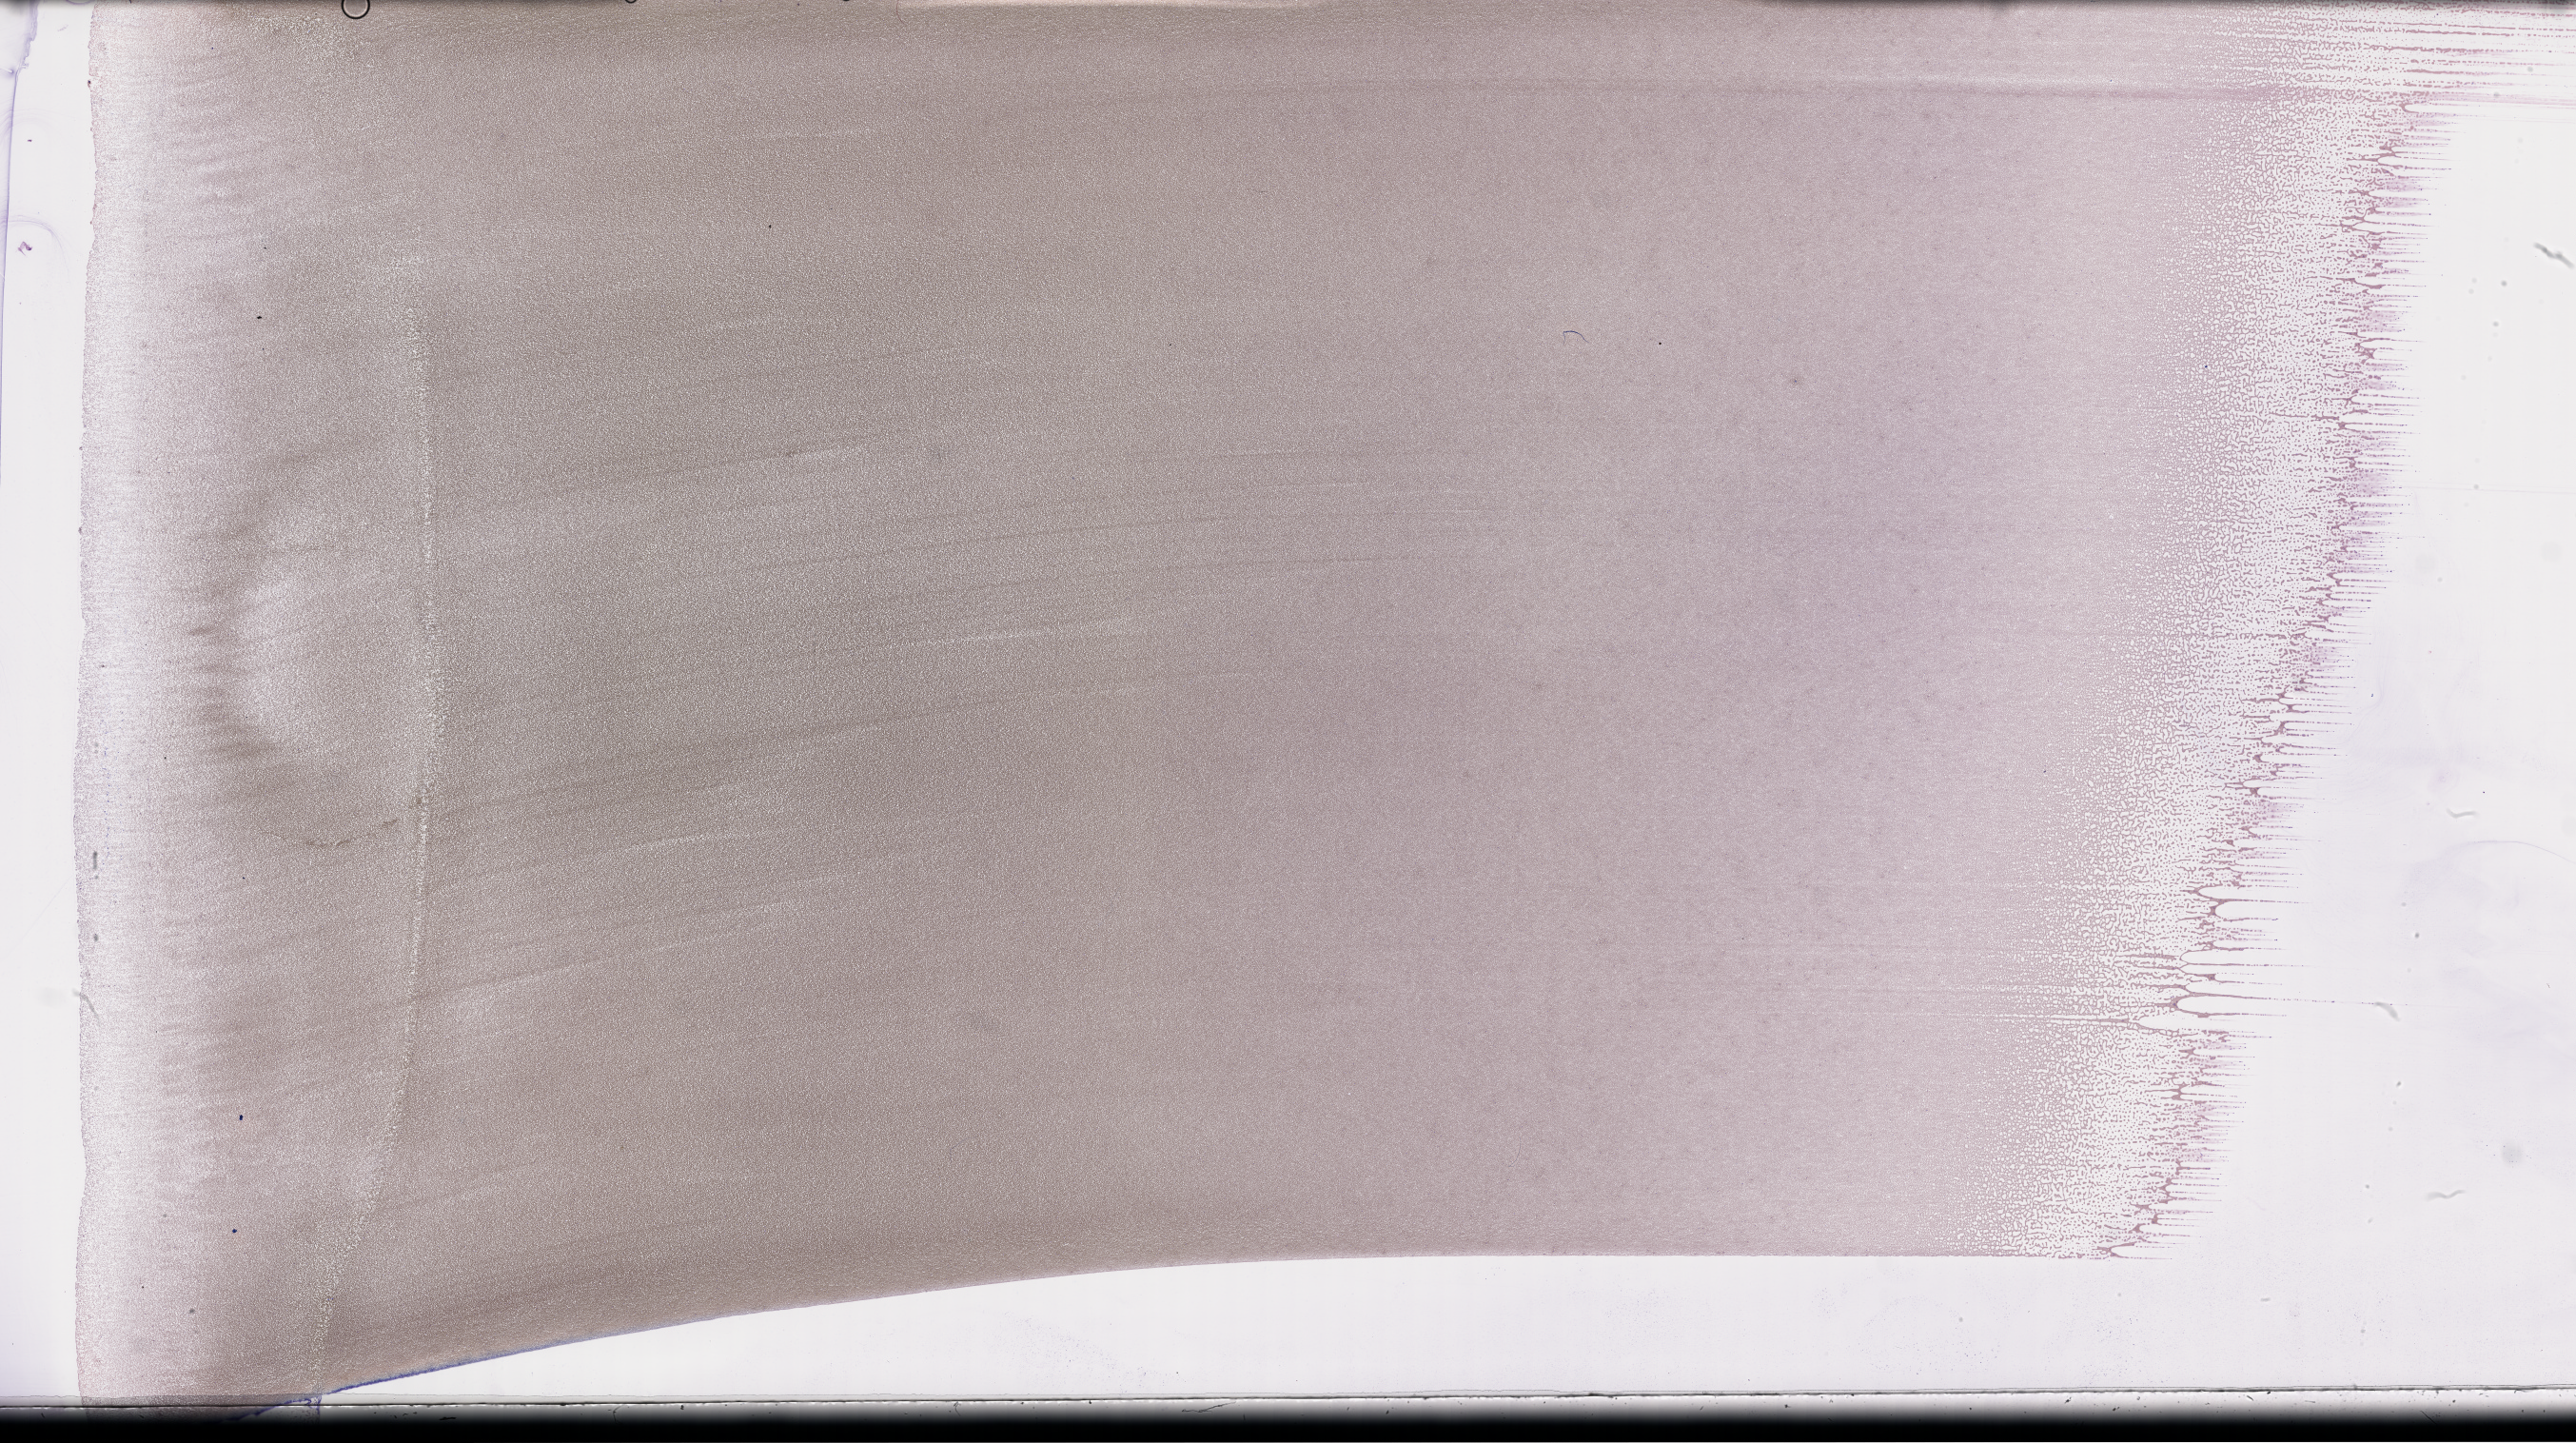
Wright-Giemsa-stained whole blood smear, whole-slide image, shown as a low-resolution overview of the whole scanned area (about 43.7 x 24.5 mm). Smear from an EDTA sample. Collected on treatment. Male patient.
From a patient with: Plasma Cell Myeloma.